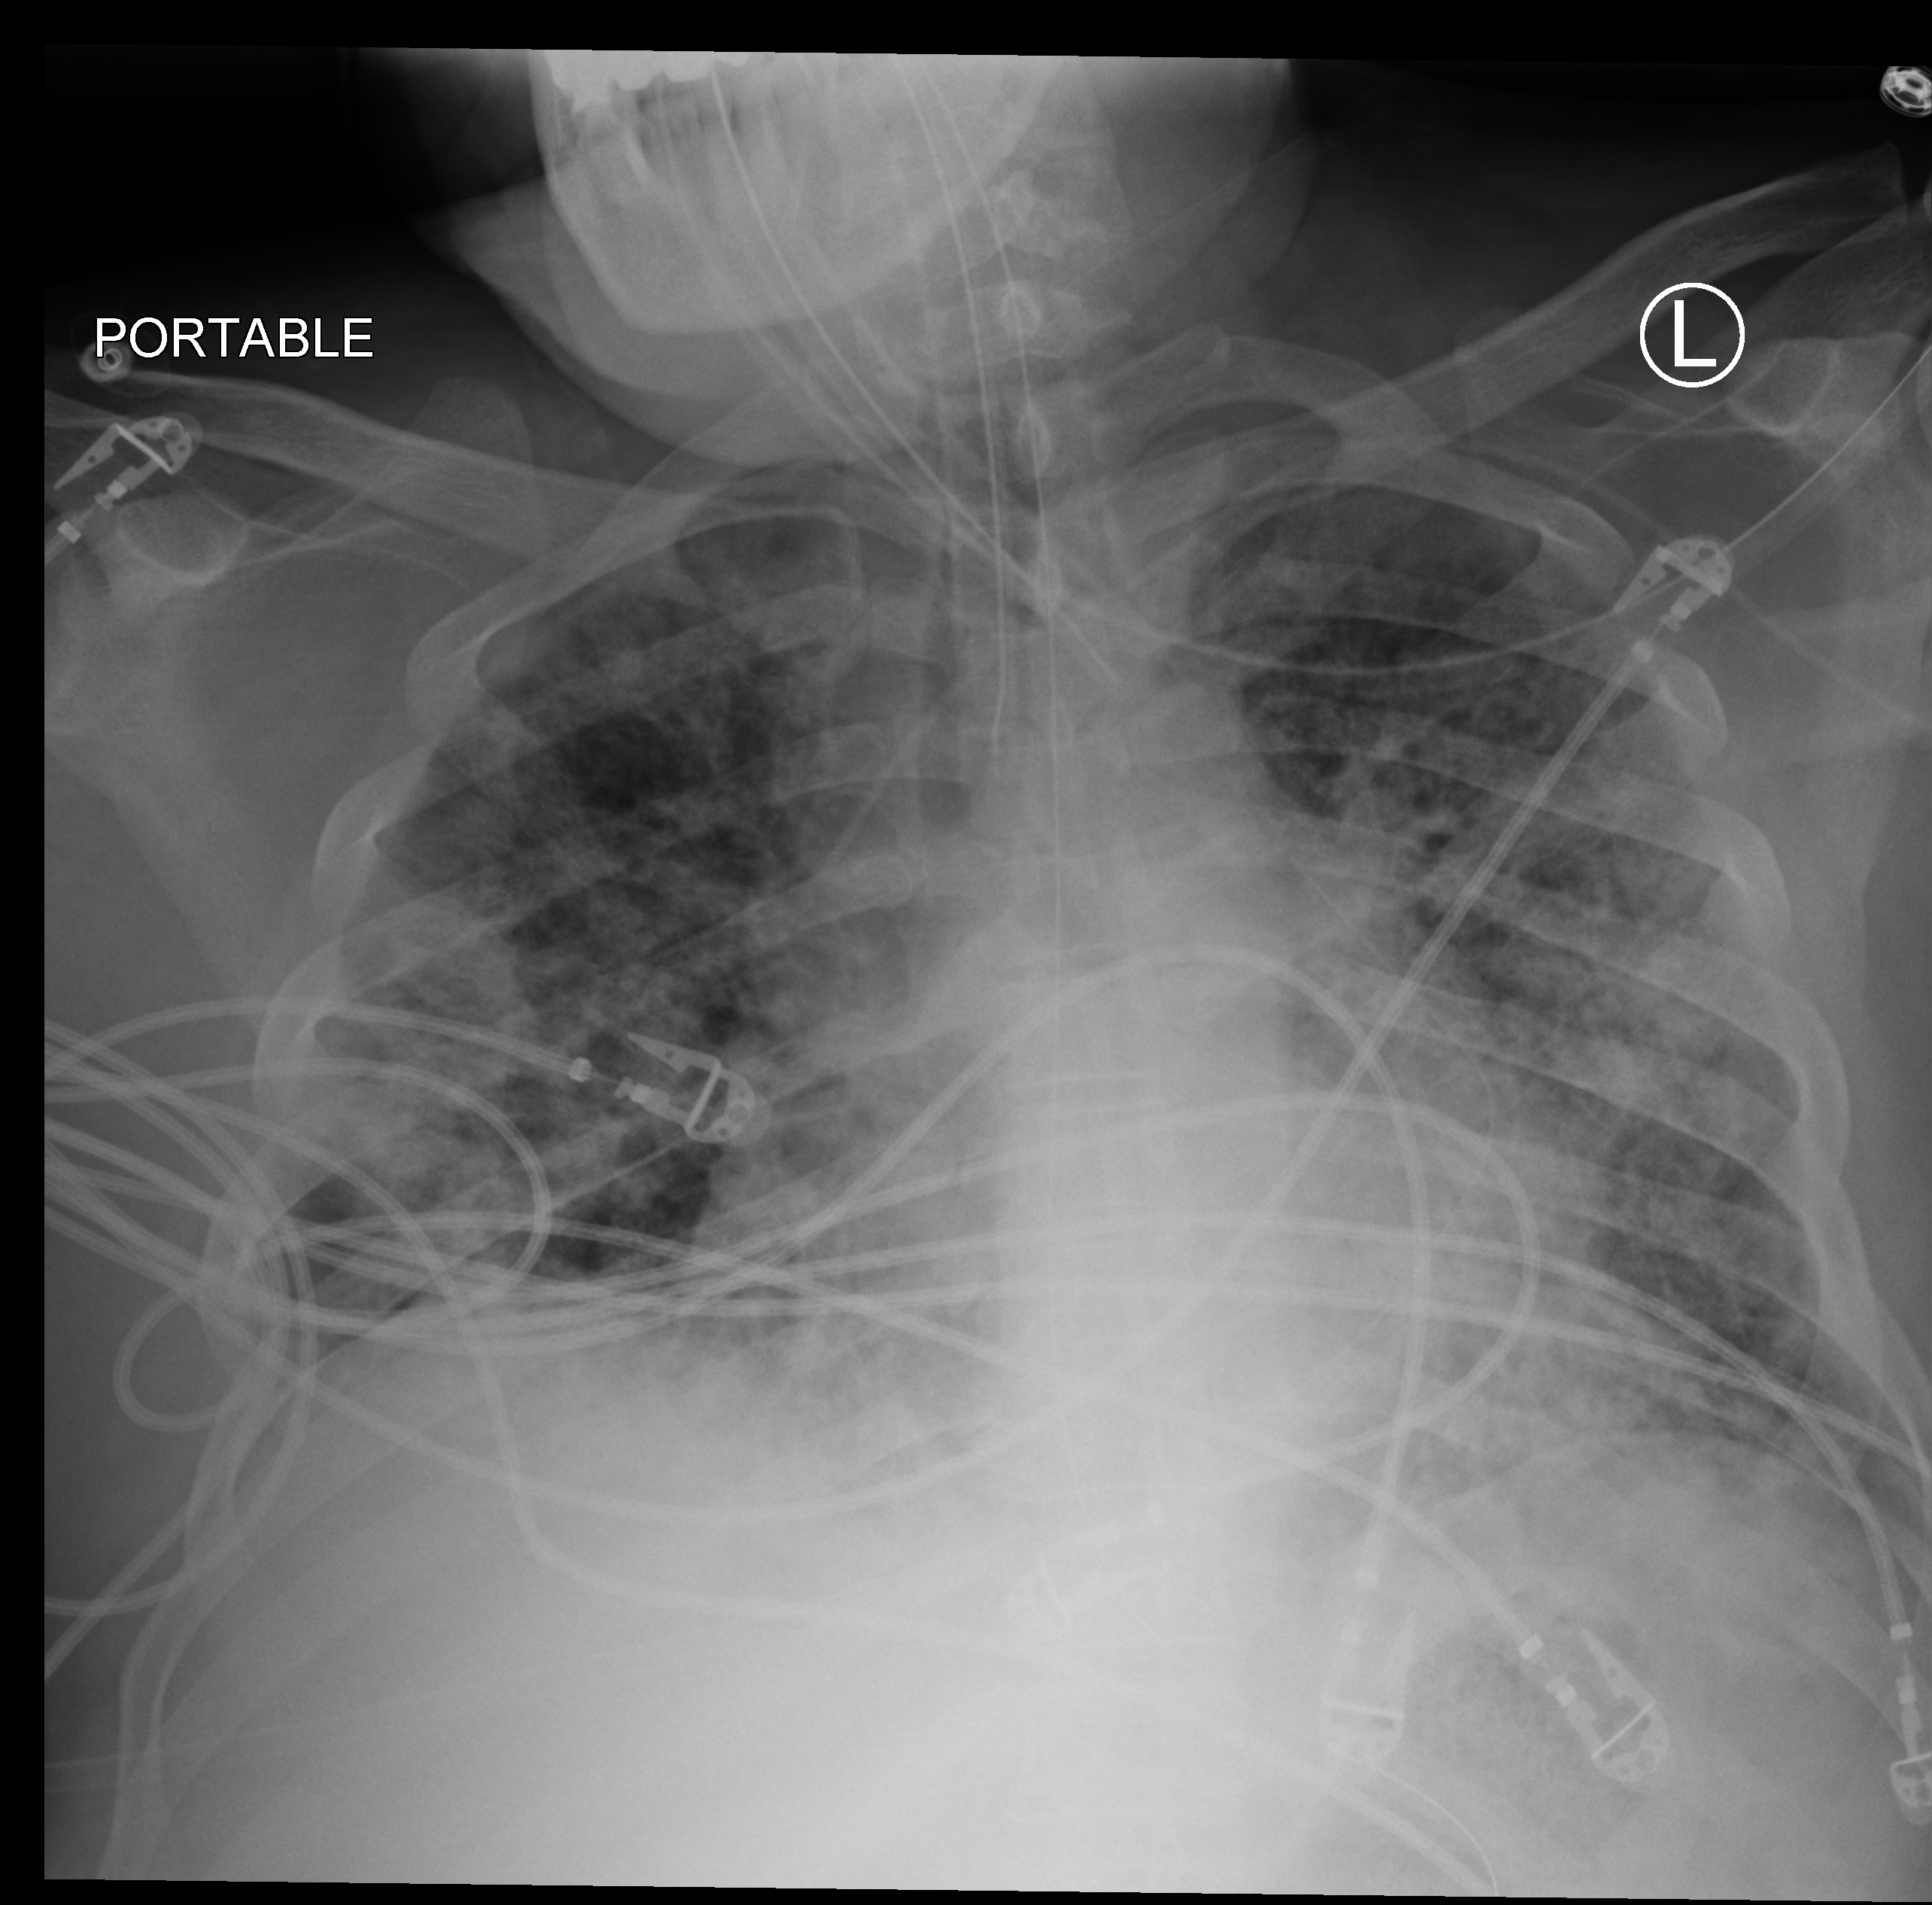
Bedside chest radiograph (computed radiography). Patient hospitalised with COVID-19; male, aged 18–59 years.
Admission-level facts for this patient (not findings on this image; timing relative to this image not recorded): admitted to intensive care during this hospital stay: yes; hypertension (admission record): no; length of hospital stay: 26 days.